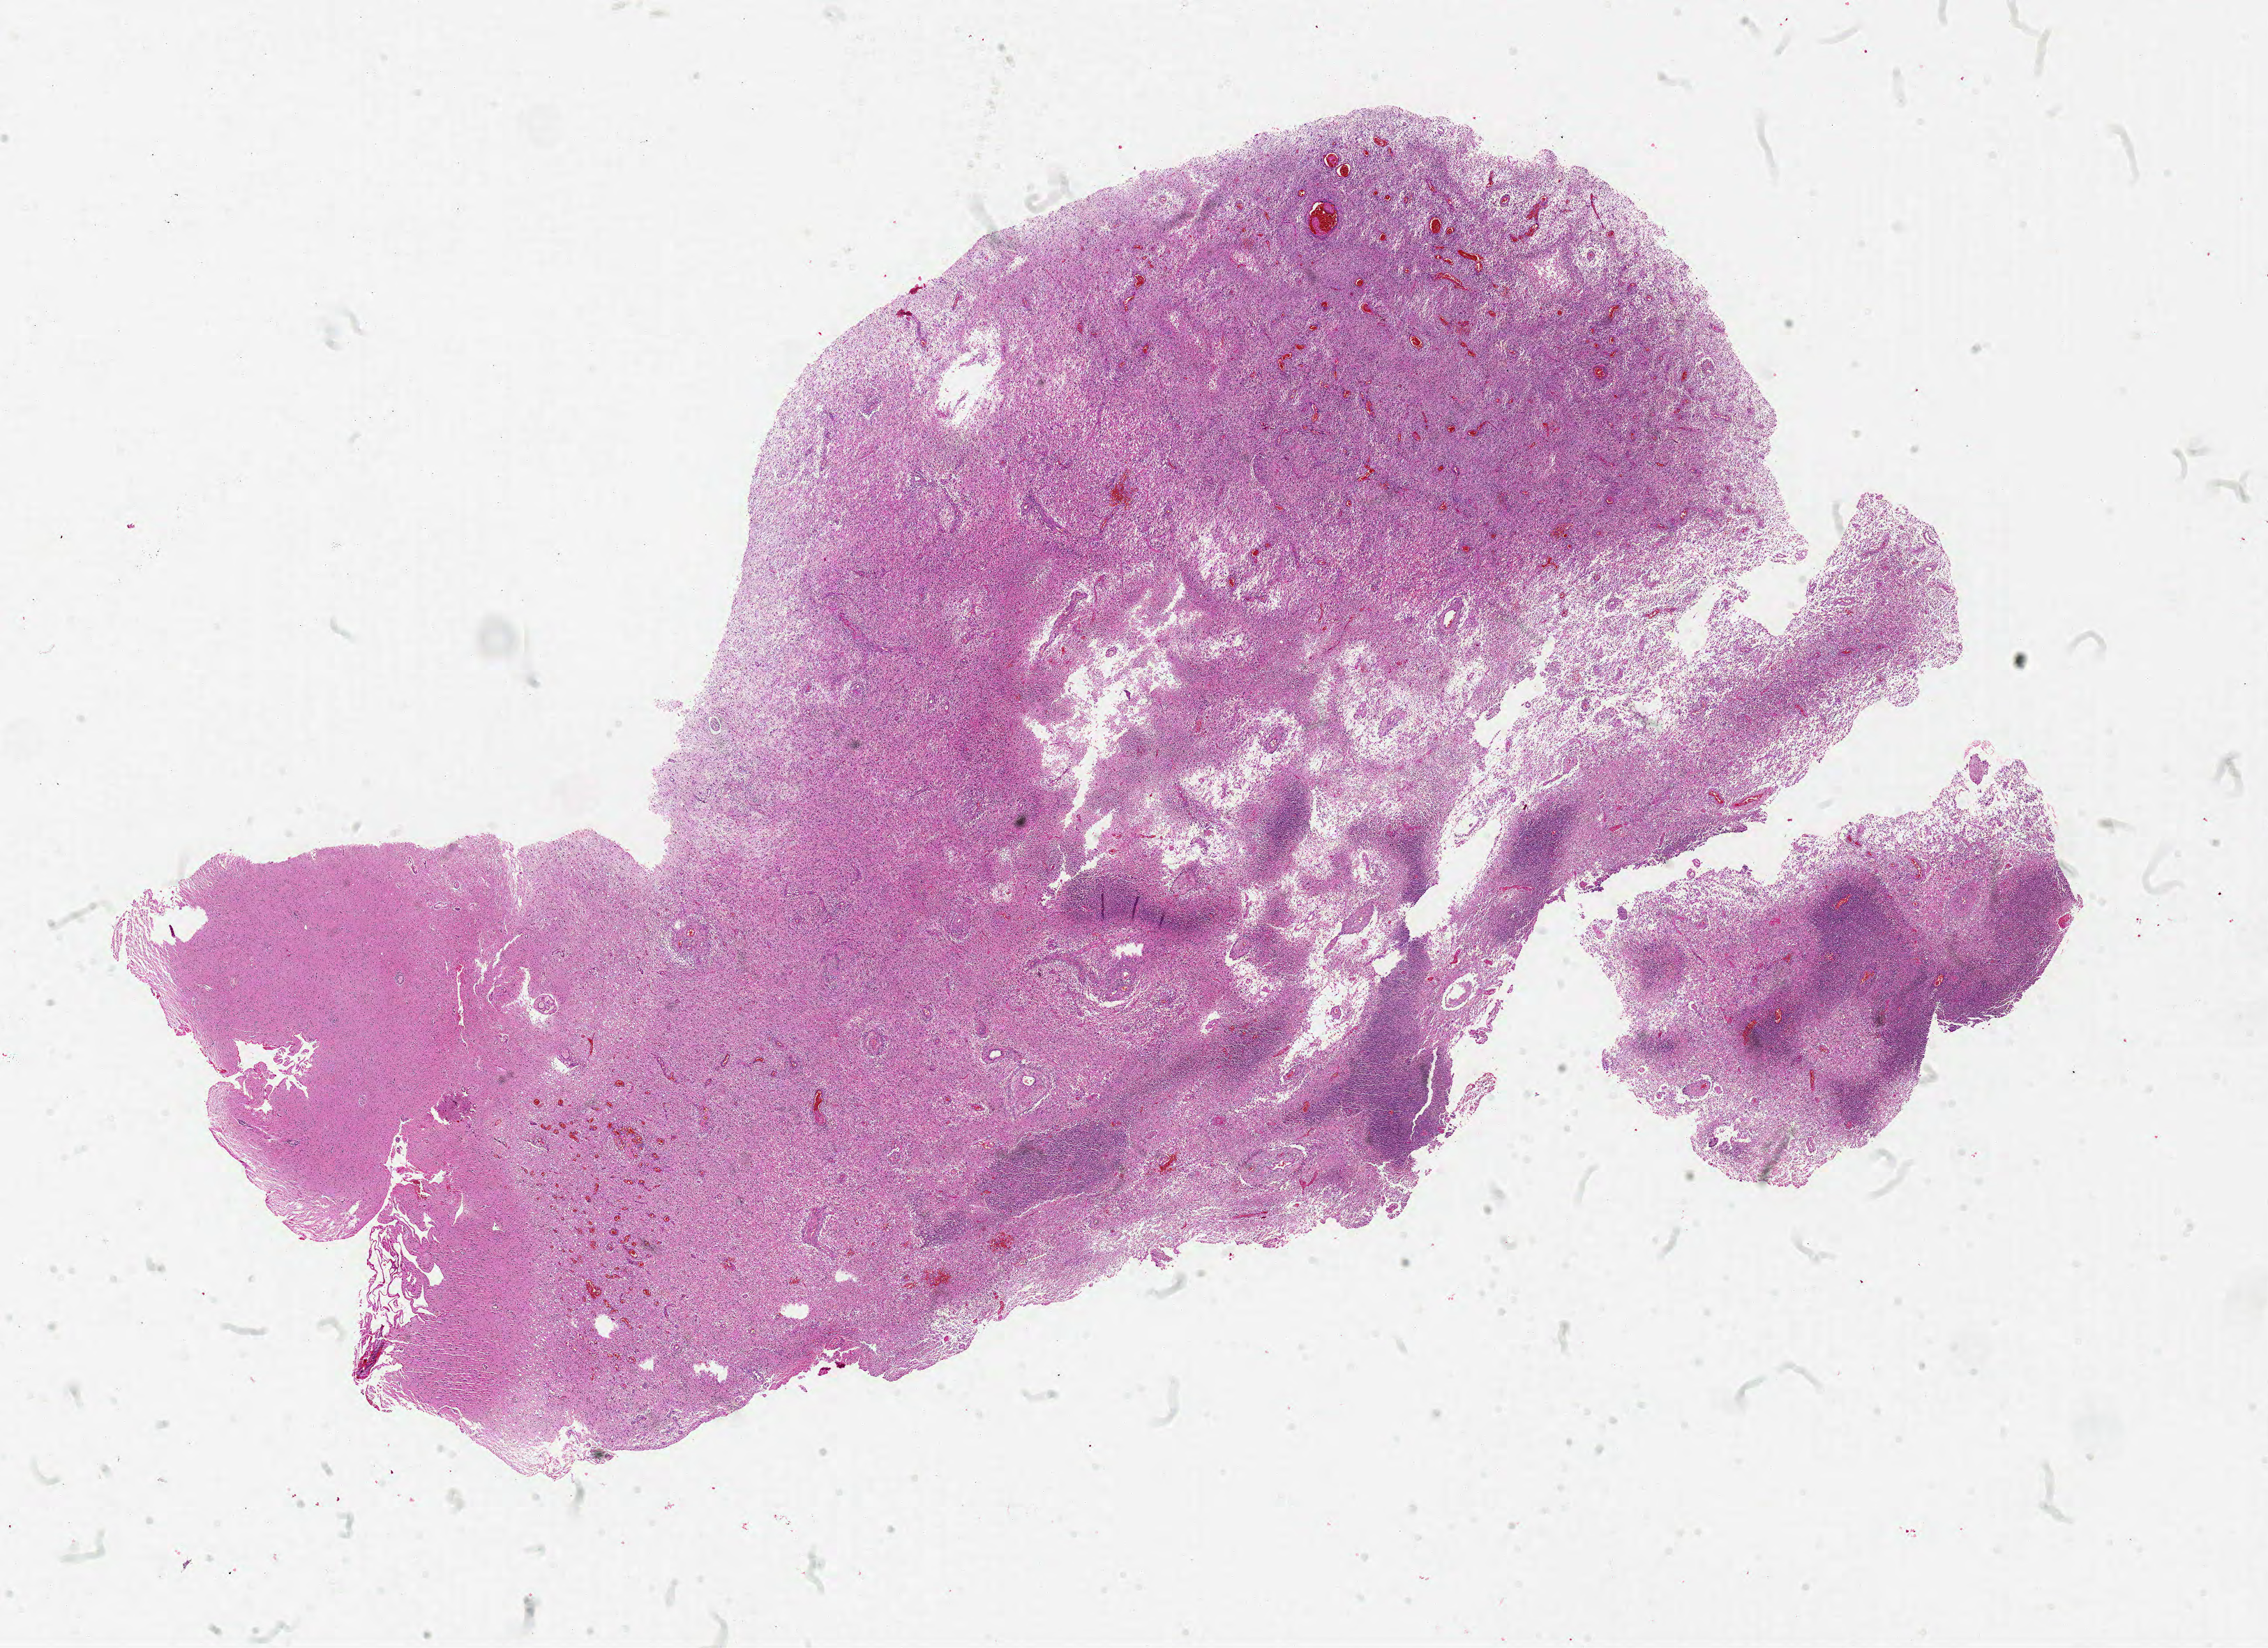
Whole-slide histology image, H&E, low-resolution overview of the scanned area, about 26.0 x 18.9 mm (acquisition: 20x scan); FFPE section; sample: primary tumour, brain. Patient: female, age at initial diagnosis 75 years.
* pathologic diagnosis: Glioblastoma